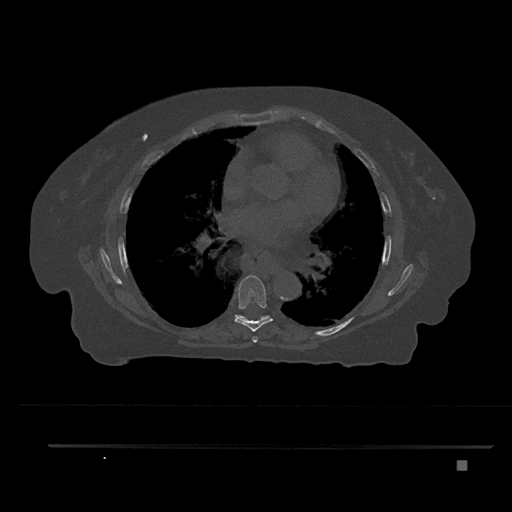
CT including the spine, one axial slice; position 483 of 797 along the scan axis; 120 kVp; bone window (W 1800 / L 400 HU); 0.5 mm slice thickness; 512 × 512 image matrix, field of view 437 × 437 mm. Patient: female, 76 years. Case-level facts recorded for this patient, not image findings: primary cancer: lung; vertebrae with lytic lesions (as recorded): T11, L3.
Structures marked on this image (semi-automatically segmented with operator editing):
- T6 vertebra: bounding box (x1, y1, x2, y2) in pixels: (252, 336, 258, 343)
- T7 vertebra: (234, 275, 273, 332)
- T8 vertebra: (237, 315, 270, 320)